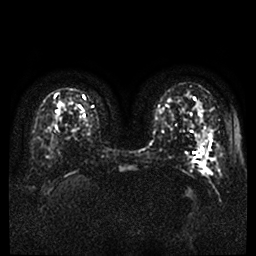
Breast MRI, one axial slice. Slice 20 of 48 in the series (ordered by position). Diffusion-weighted series; image 2 of 4 stored at this slice position (different b-values; order by instance number). 1.5 T. 4 mm slice thickness. 256 × 256 image matrix, field of view 360 × 360 mm. Female patient.
Annotated regions visible in this slice (manually delineated by an expert):
- tumour on diffusion-weighted imaging: box from (x=199, y=150) to (x=212, y=174) px